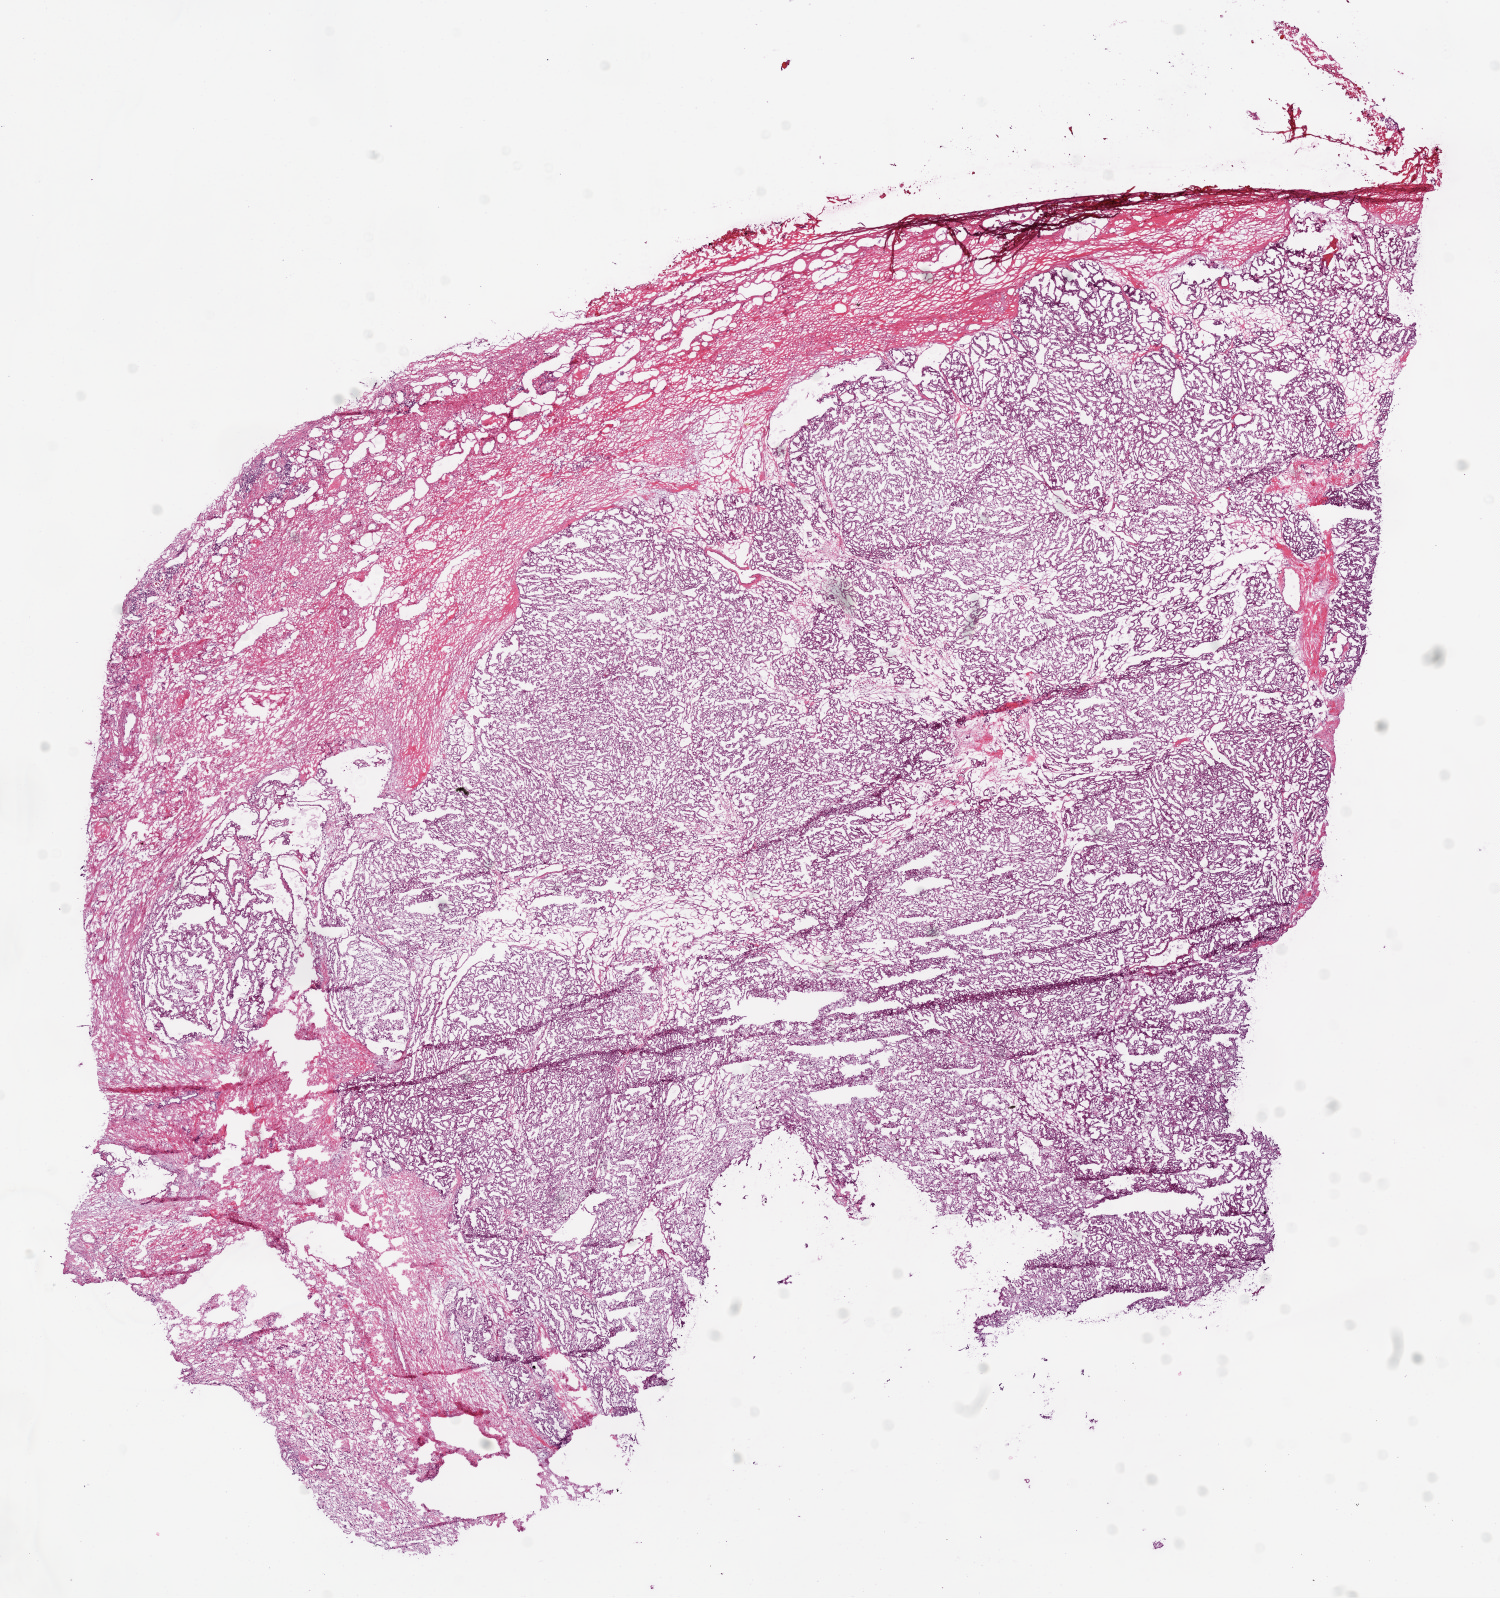
Digitized H&E tissue section (whole slide), low-resolution overview of the scanned area, about 12.0 x 12.8 mm; frozen section; primary tumour sample from the kidney. Male, age 65 years at initial diagnosis. Histologic grade: G2 (moderately differentiated). Composition of this section per pathologist review: tumour cells 60%, tumour nuclei 80%, normal cells 20%, stromal cells 20%, necrosis 0%.
• AJCC pathologic stage: I
• laterality: right
• diagnosis: Clear cell adenocarcinoma, NOS